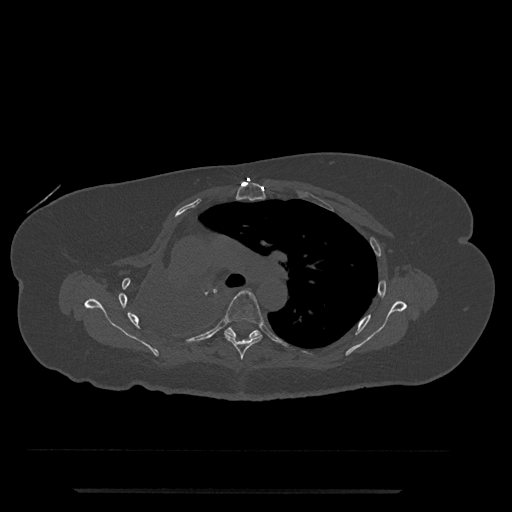
CT including the spine, one axial slice. Slice 528 of 797 in the series (ordered by position). Reconstruction kernel Br40s/3. 120 kVp. Bone window (W 1800 / L 400 HU). 0.5 mm slice thickness. 512 × 512 image matrix. Patient: female, 51 years. Case-level facts recorded for this patient, not image findings: primary cancer: neuro; vertebrae with lytic lesions (as recorded): T8.
Annotated regions visible in this slice (semi-automatic segmentation, software-assisted and operator-edited):
- T5 vertebra: box from (x=224, y=290) to (x=264, y=360) px
- T6 vertebra: (x=225, y=327)–(x=273, y=340)